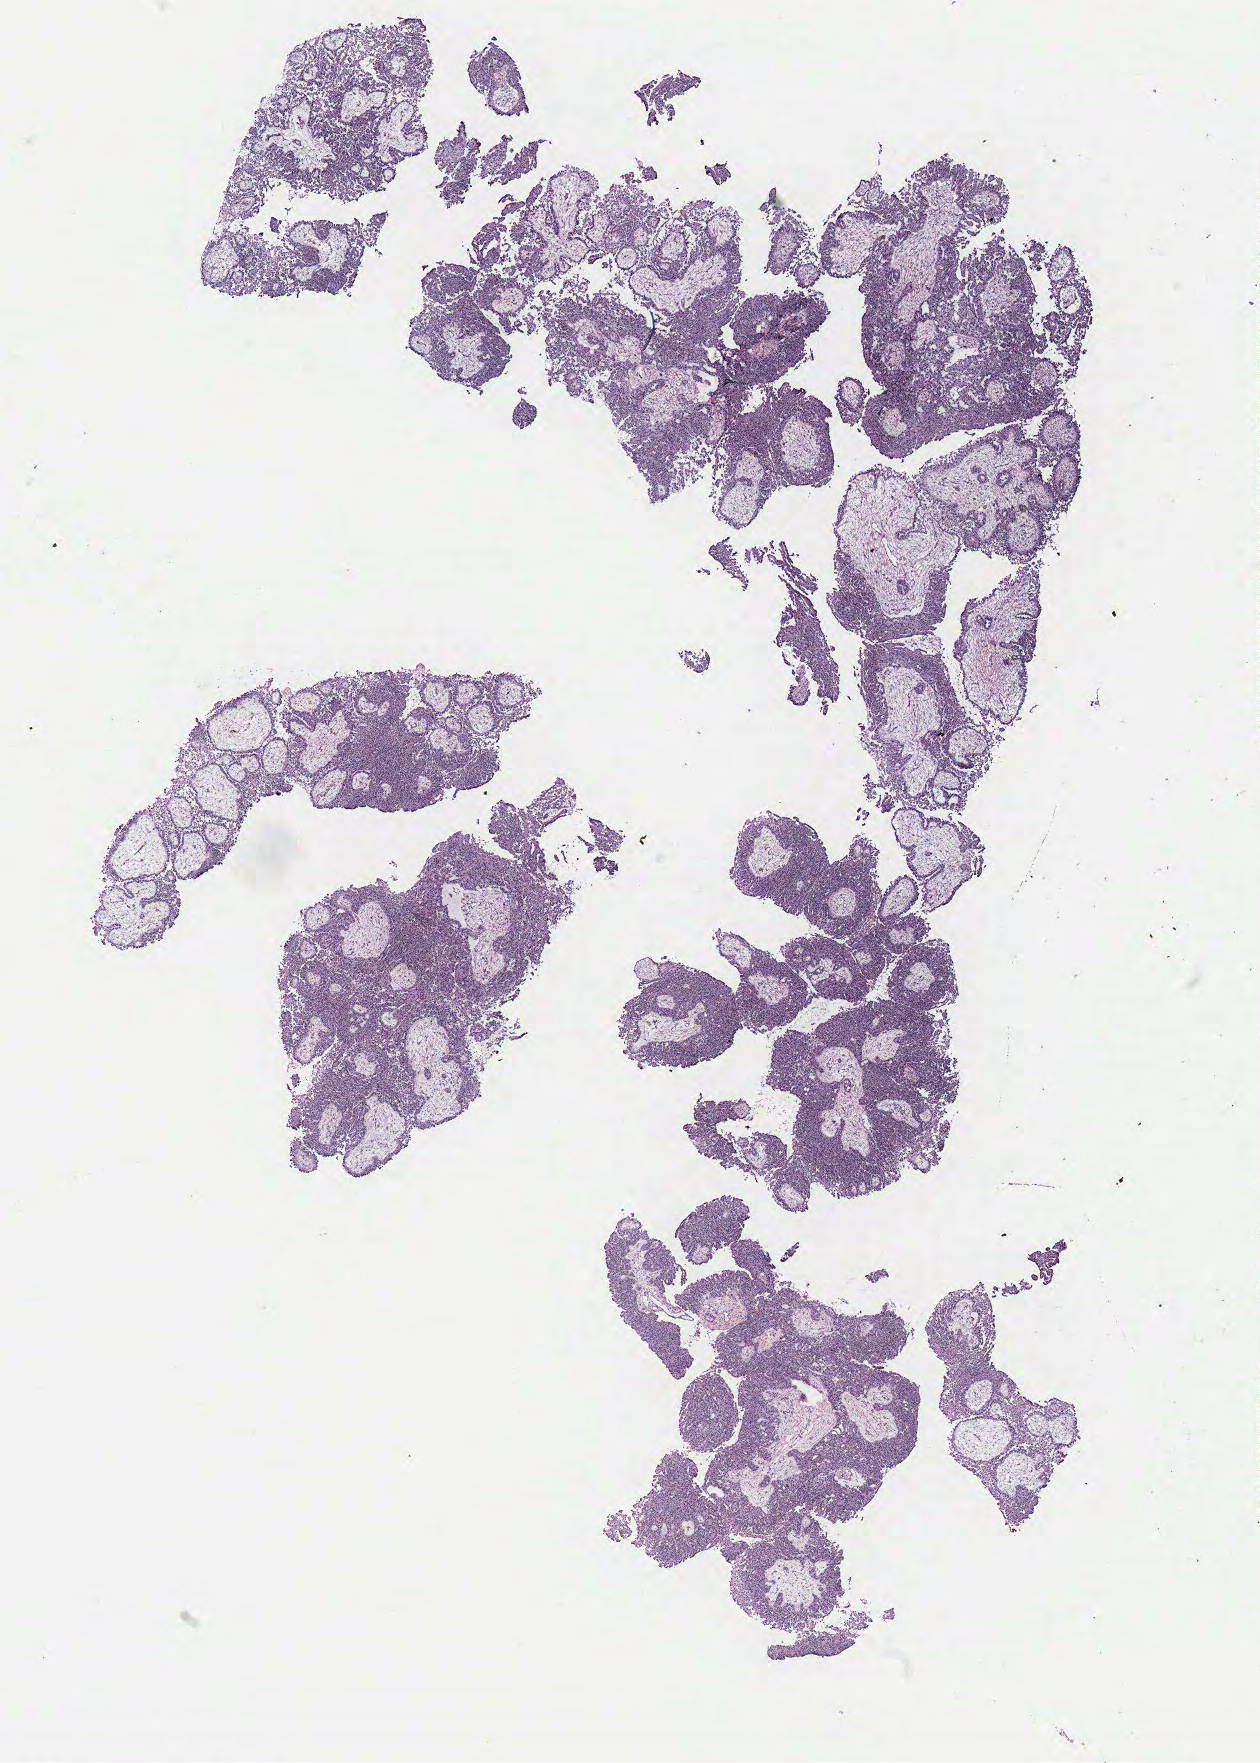
H&E whole-slide image — low-resolution overview of the scanned area, about 10.1 x 14.1 mm (slide scanned at 40x). Tumour tissue sample, ovary. Female, 85 y/o.
Primary tumour site (as recorded): fallopian tube. Histologic diagnosis: Serous adenocarcinoma, NOS.